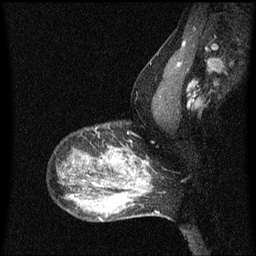
Breast MRI (dynamic contrast-enhanced), one sagittal slice. Slice 45 of 60 in the series (ordered by position). Dynamic contrast-enhanced series, image 2 of 3 at this slice position (ordered by acquisition). 1.5 T. TE 4.2 ms, TR 8 ms. 2 mm slice thickness. 256 × 256 image matrix. Patient: female, 50 years.
Annotated regions visible in this slice (semi-automatic segmentation, software-assisted and operator-edited):
- analysis volume of interest (the breast-tissue region the enhancement analysis was run in; not a lesion): bounding box <91,146,141,189> (left, top, right, bottom; pixels)
- tumour enhancement mask (voxels above the 70 % enhancement threshold inside the analysis volume of interest): <114,154,125,173>